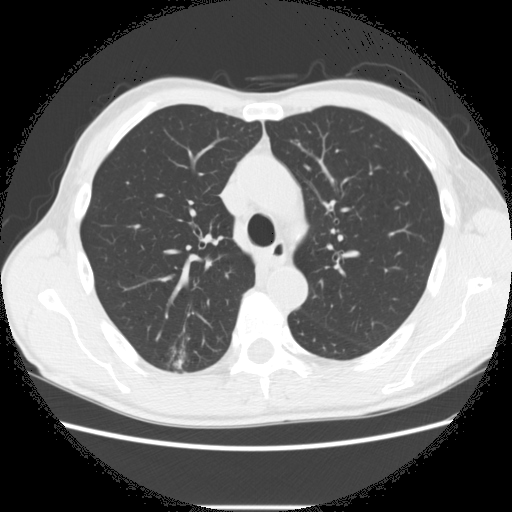
Low-dose screening chest CT, axial slice; second screening round (one year after baseline); lung window (W 1500 / L -600 HU); 2.5 mm slice thickness; standard (soft-tissue) reconstruction kernel (STANDARD); slice 86 of 282 in the series. Male participant, aged 66 years at enrolment.
Expert-annotated lung lesion, bounding box (x1, y1, x2, y2) in pixels: (164, 342, 219, 383). The screening reader recorded 5 non-calcified nodules or masses ≥4 mm on this exam (right lower lobe, right upper lobe, right upper lobe, right upper lobe, left lower lobe); which of them this box marks is not recorded. Official screen result: positive, change unspecified: nodule(s) >= 4 mm or enlarging nodule(s), mass(es), or other non-specific abnormalities suspicious for lung cancer. Participant outcome: lung cancer diagnosed 75 days after this screen — adenocarcinoma, NOS, right upper lobe, undifferentiated (G4), stage IA (AJCC 6th edition), 20 mm at pathology.